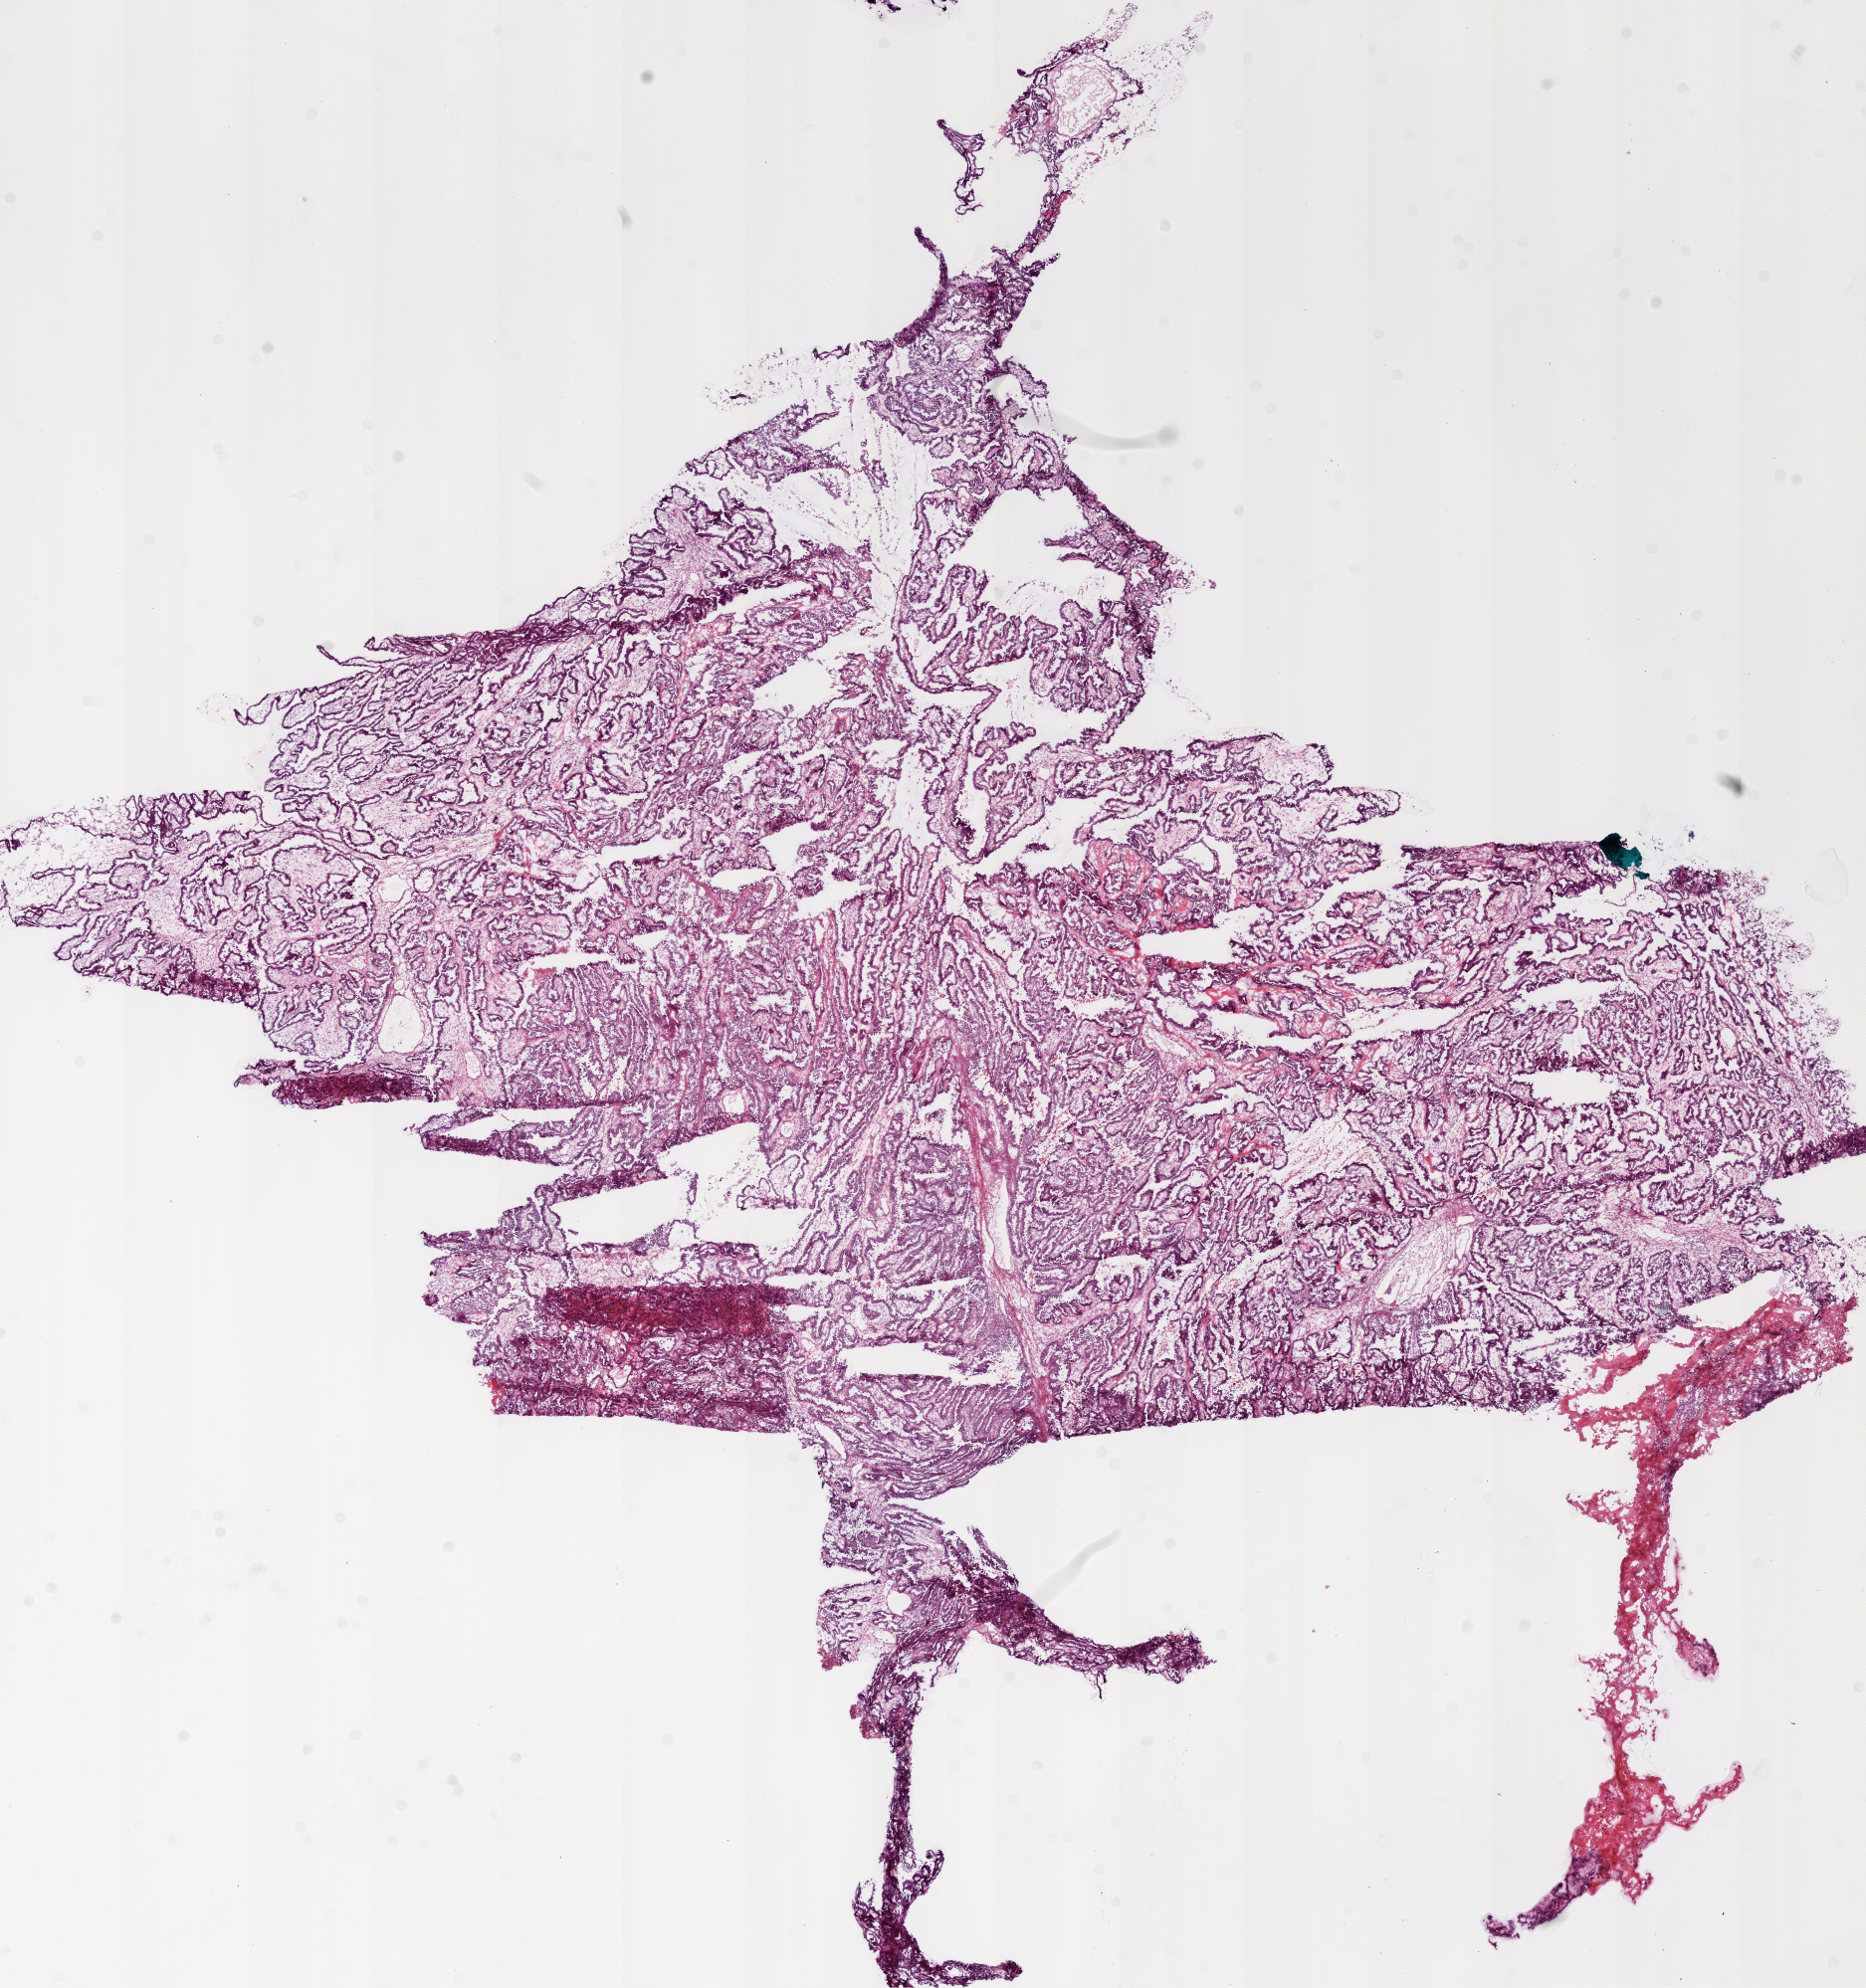
Whole-slide histology image, H&E, a low-resolution overview of the entire scanned area, about 15.0 x 16.0 mm (acquisition: 20x scan); frozen section from the bottom of the tissue portion; primary tumour sample from the ovary. Female patient; age at initial diagnosis 51 years. Histologic grade: G3 (poorly differentiated). Slide review estimates, as recorded: tumour cells 80%, tumour nuclei 80%, normal cells 0%, stromal cells 19%, necrosis 1%.
- diagnosis: Serous cystadenocarcinoma, NOS
- FIGO stage: IIIC
- laterality: right